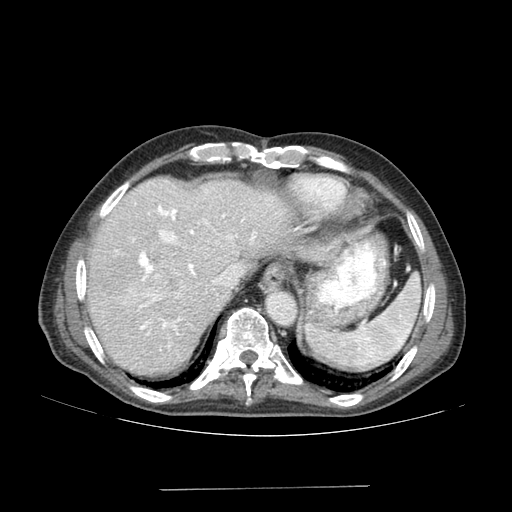
Contrast-enhanced abdominal CT (liver protocol), one axial slice; position 134 of 192 along the scan axis; 120 kVp; soft-tissue window (W 400 / L 40 HU); 2.5 mm slice thickness; 512 × 512 image matrix. From the clinical record (not read from this slice): diagnosis: hepatocellular carcinoma (patient treated with transarterial chemoembolisation; whether this scan precedes or follows treatment is not stated here); TNM stage (as recorded): Stage-IVA; Child-Pugh class: A; tumour differentiation: poorly differentiated.
Annotated regions visible in this slice (semi-automatic segmentation, software-assisted and operator-edited):
- abdominal aorta: bounding box [x1, y1, x2, y2] px = [266, 292, 295, 323]
- liver parenchyma outside the tumour (the mass and vessels are separate outlines, so this box may not span the whole liver): [86, 178, 313, 374]
- mass: [133, 266, 178, 303]
- liver vessels: [129, 191, 297, 336]